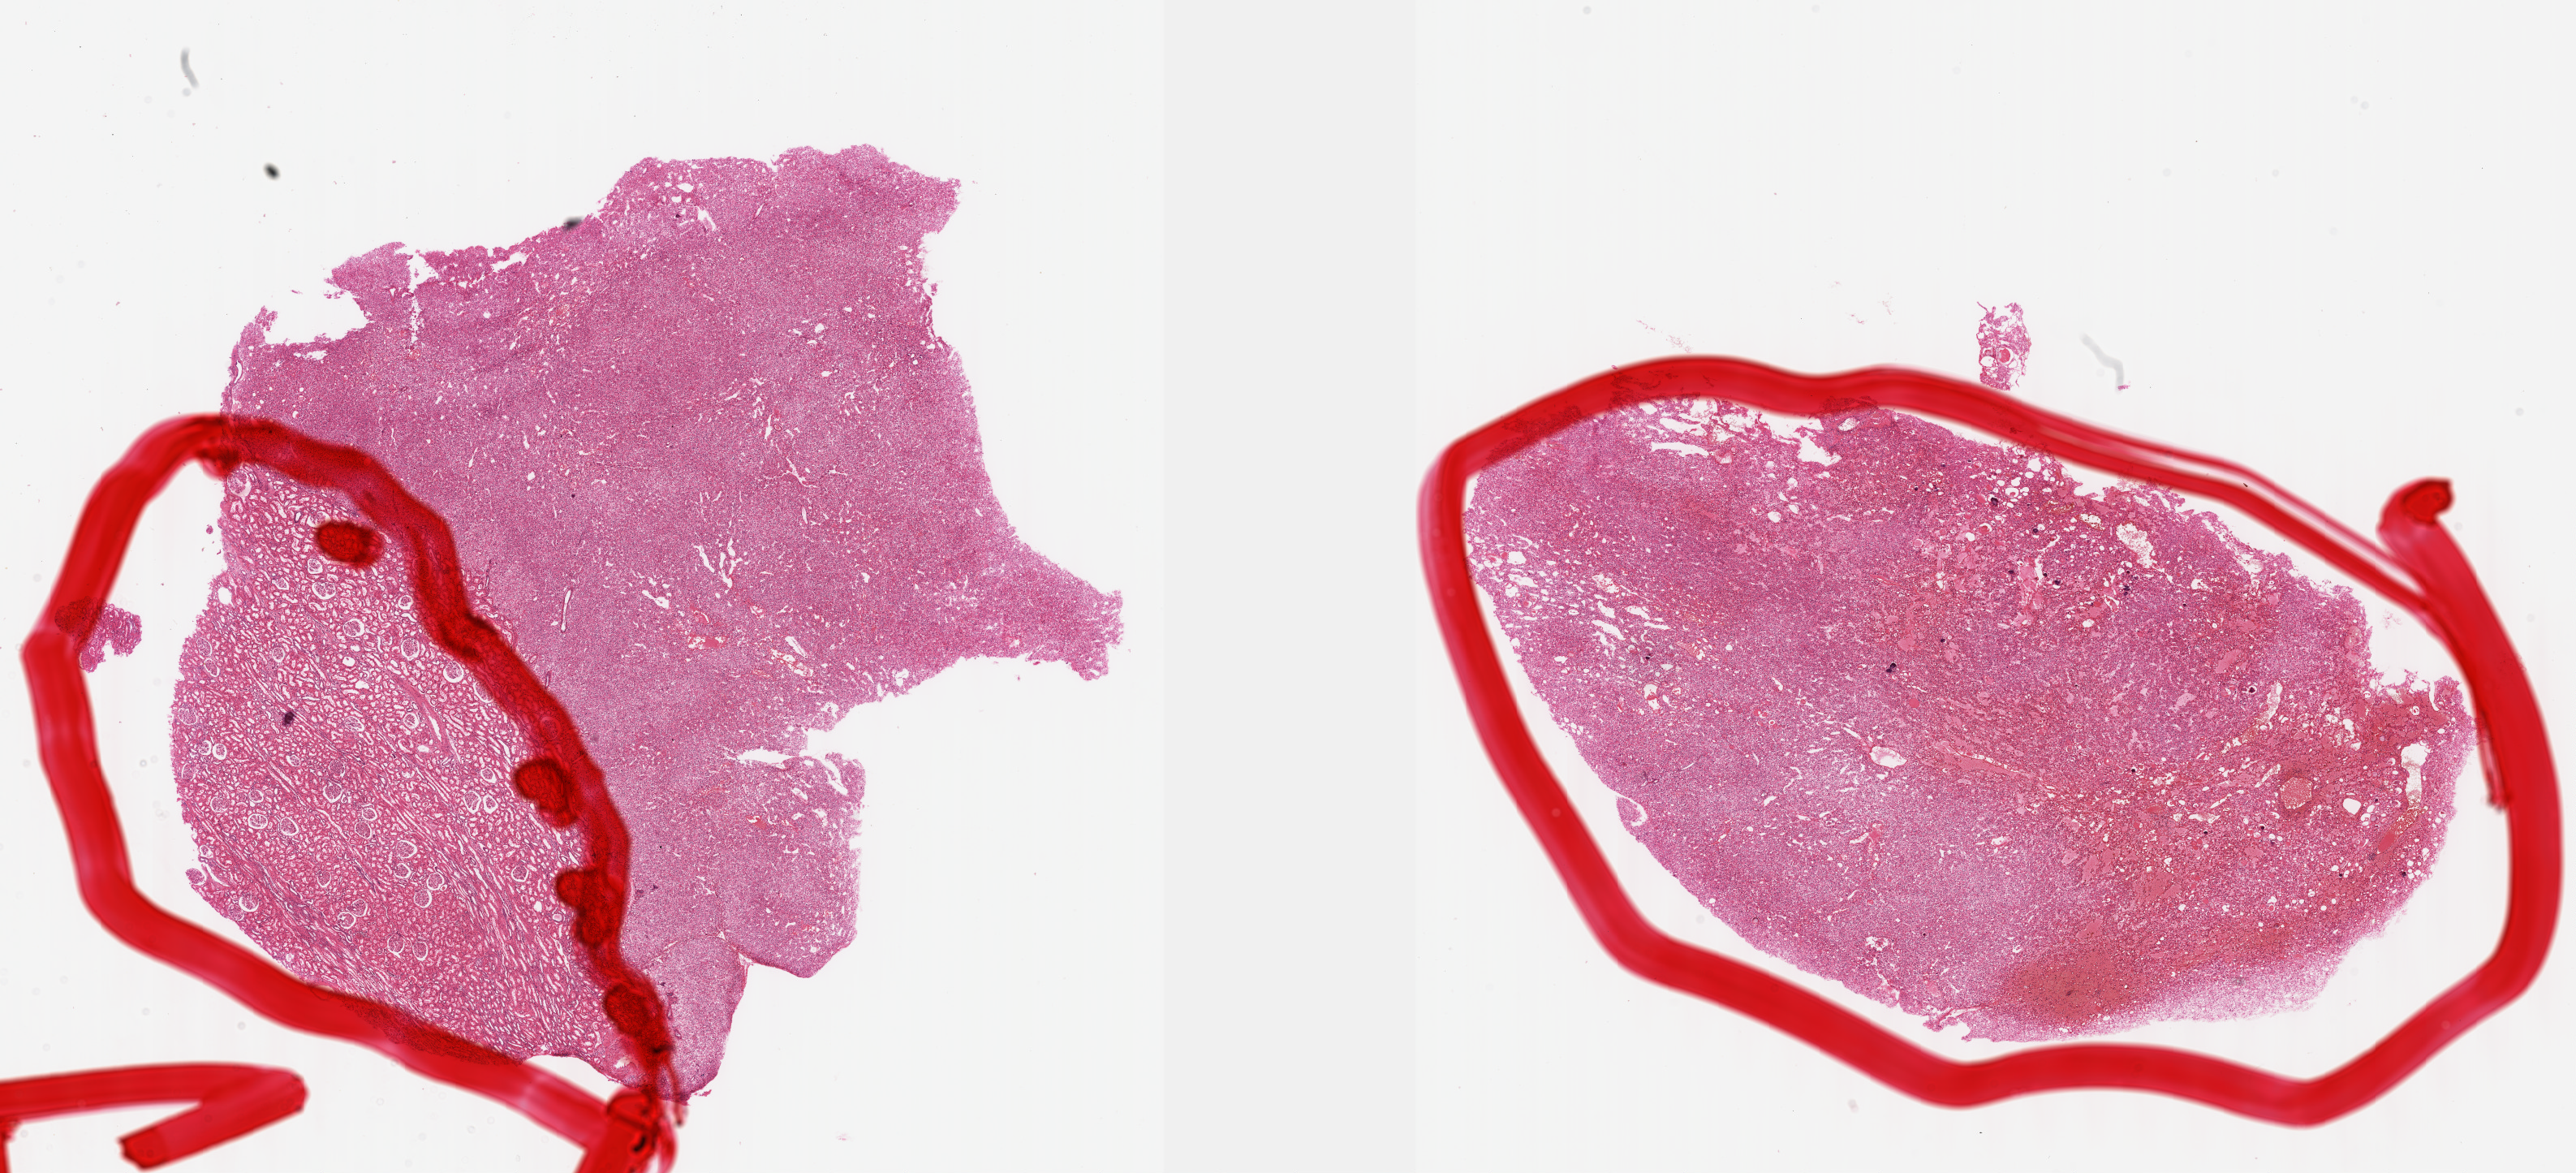
H&E whole-slide image — whole scanned area (about 25.7 x 11.7 mm) shown as a low-resolution overview, FFPE section, kidney, primary tumour sample. Male patient; age at initial diagnosis 39 years. Slide review estimates, as recorded: tumour cells 65%, tumour nuclei 70%, normal cells 30%, stromal cells 5%, necrosis 0%. Inflammatory infiltration, as recorded: lymphocyte infiltration 3%, monocyte infiltration 1%, neutrophil infiltration 1%.
Diagnosis: Renal cell carcinoma, chromophobe type. Laterality: right. AJCC pathologic stage: I (5th edition).